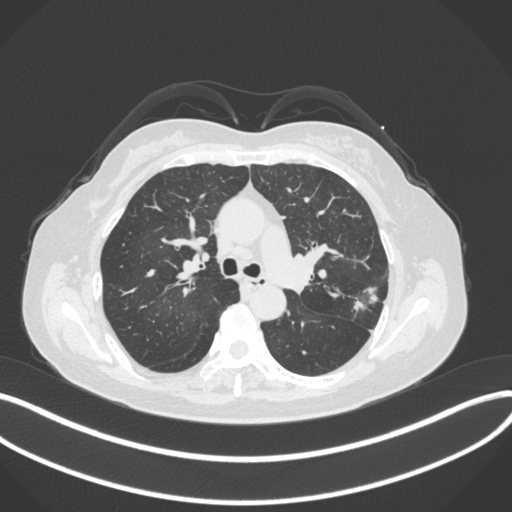
Chest CT, one axial slice. Slice 217 of 330 in the series (ordered by position). Reconstruction kernel B31f. 120 kVp. Lung window (W 1500 / L -600 HU). 512 × 512 image matrix, field of view 400 × 400 mm. Female patient, age 60 years. From the clinical record (not read from this slice): clinical TNM (as recorded): T1c N0 M0.
Annotated regions visible in this slice (rectangle marked by the reading radiologist):
- lung tumour (recorded histology: adenocarcinoma): bounding box <349,278,382,318> (left, top, right, bottom; pixels)